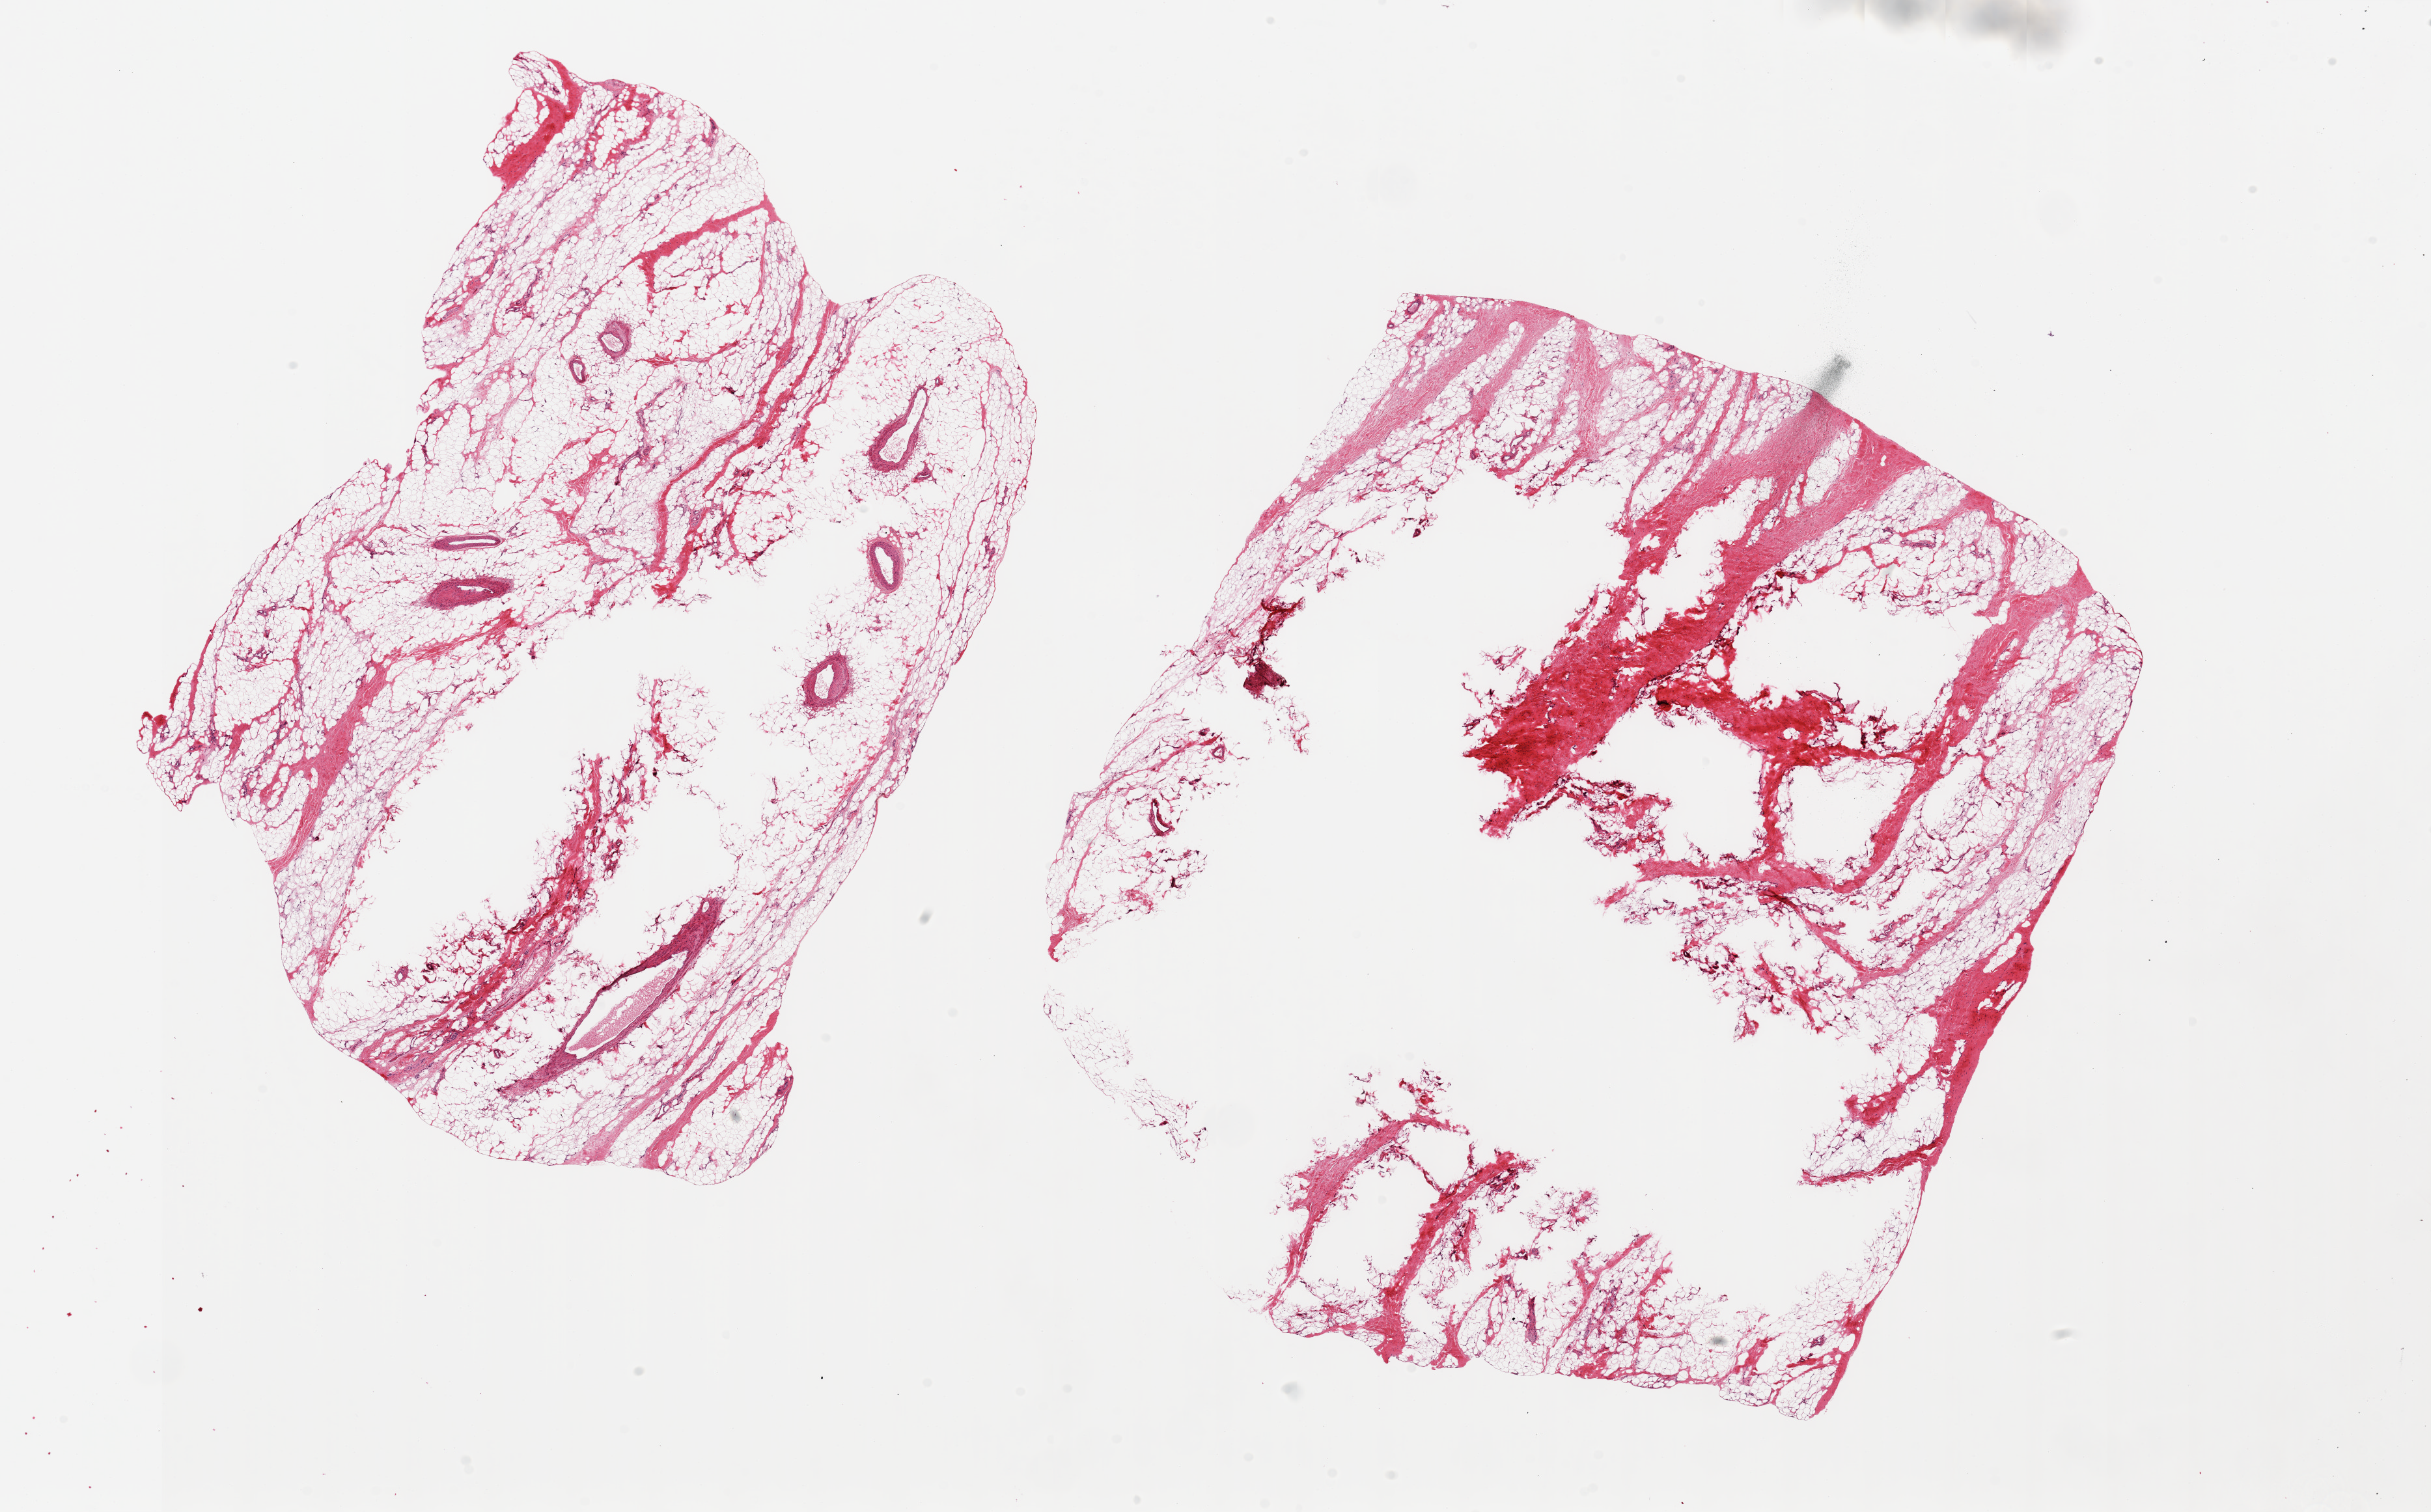
H&E whole-slide image — low-resolution overview of the scanned area, about 29.5 x 18.4 mm. PAXgene-fixed, paraffin-embedded tissue. Target tissue: skeletal muscle. Donor tissue sample. Donor: male.
• pathologist's review note for this sample: 2 pieces 12x9. All fibroadipose tissue, no skeletal muscle present